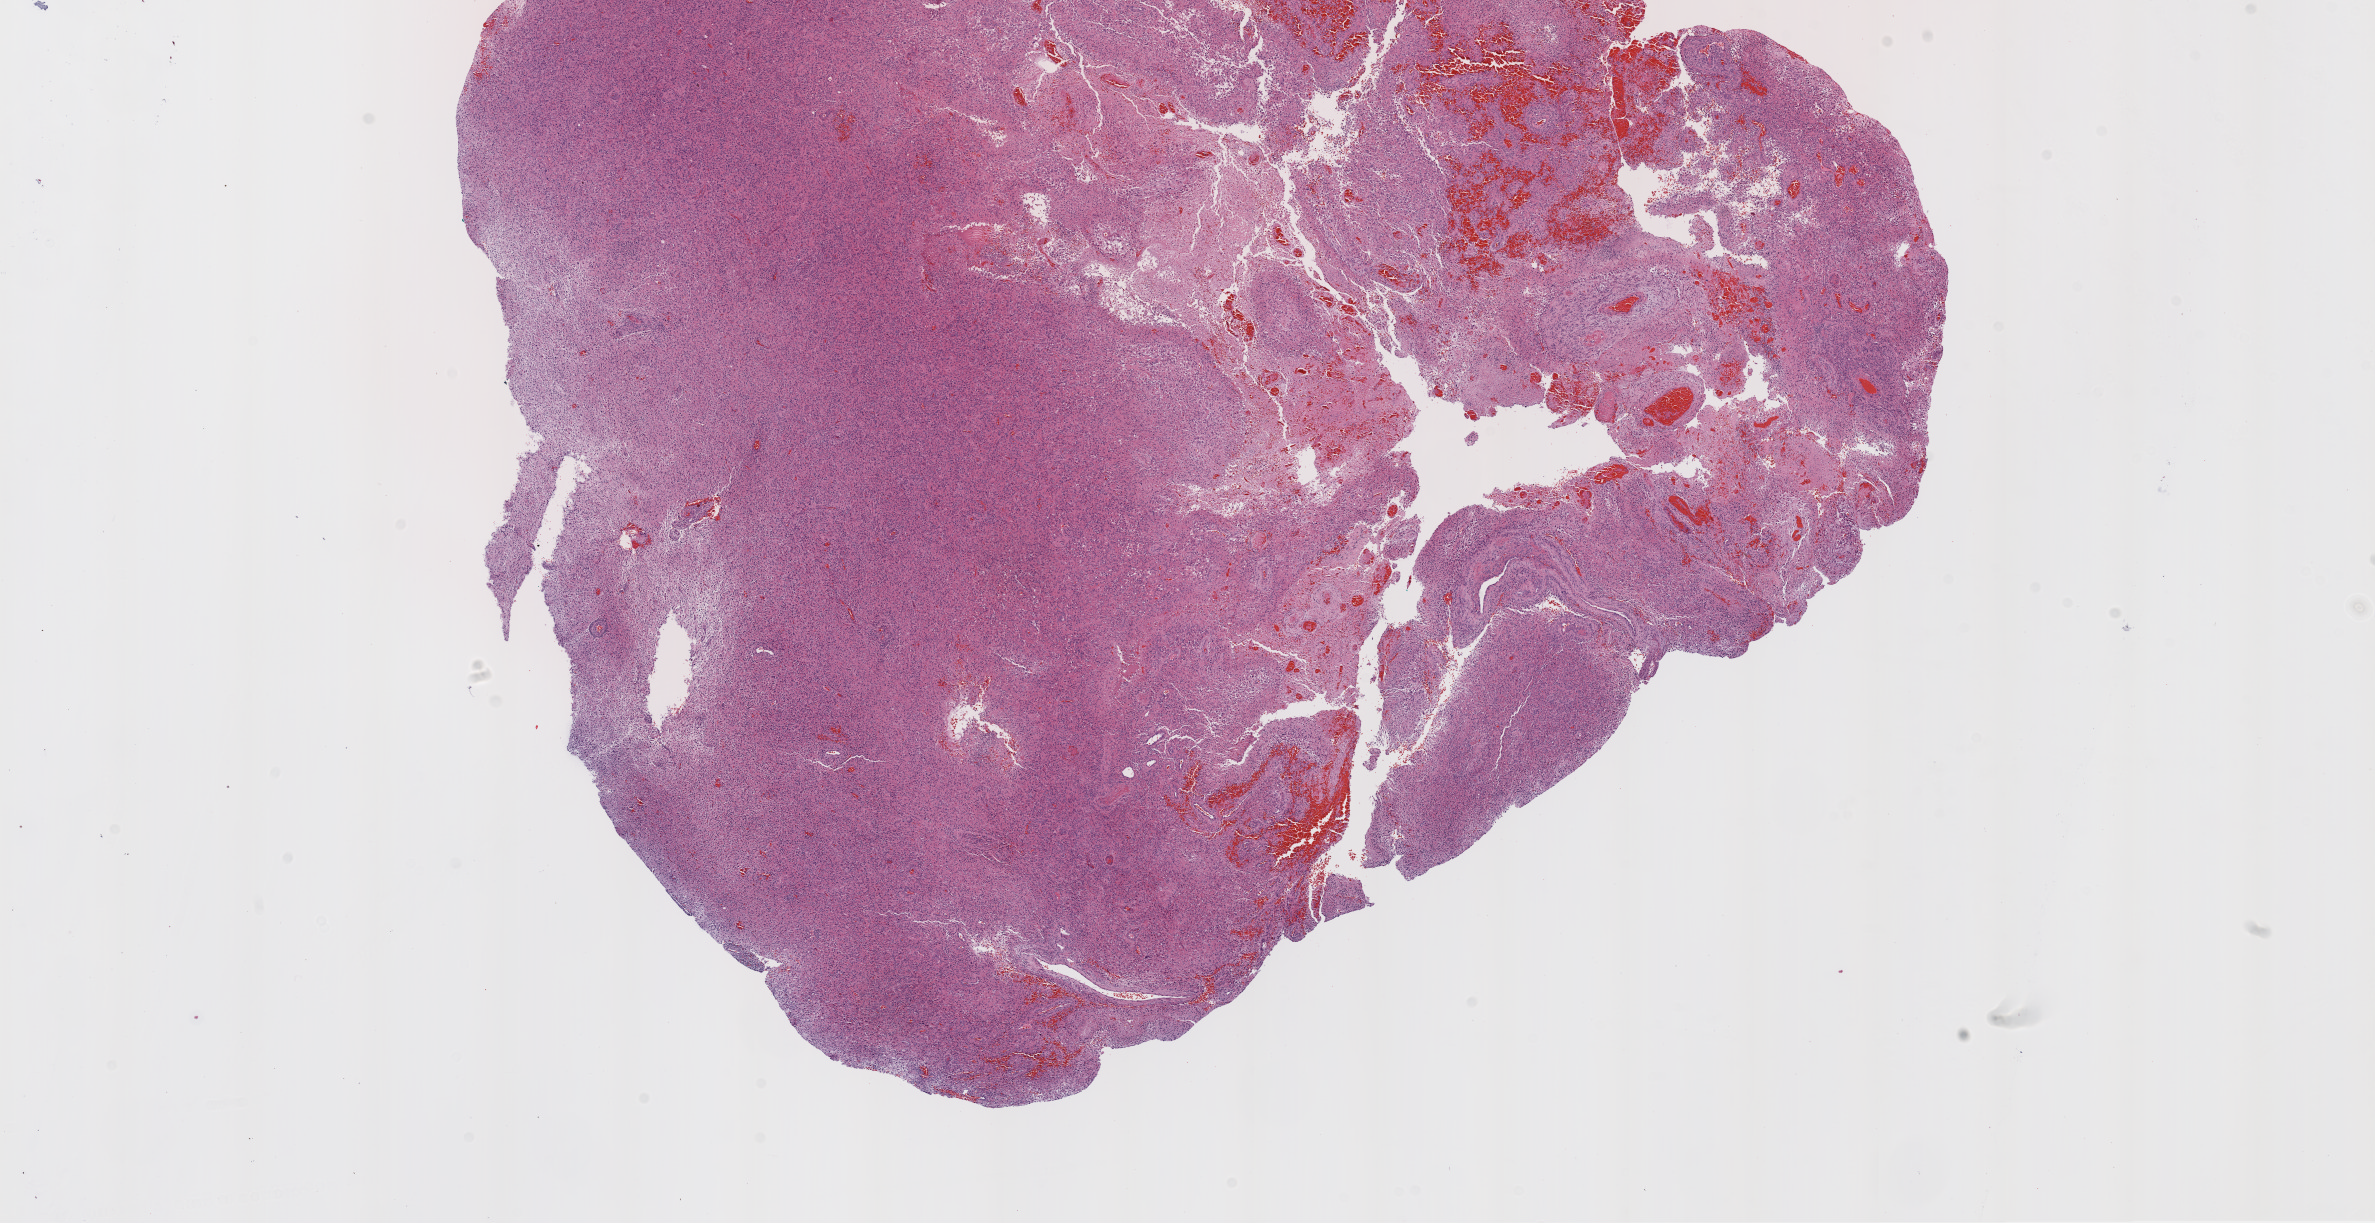
H&E-stained whole-slide image, a low-resolution overview of the entire scanned area, about 19.1 x 9.8 mm, FFPE section, primary tumour sample from the brain. Male patient; age at initial diagnosis 64 years.
Diagnosis: Glioblastoma.